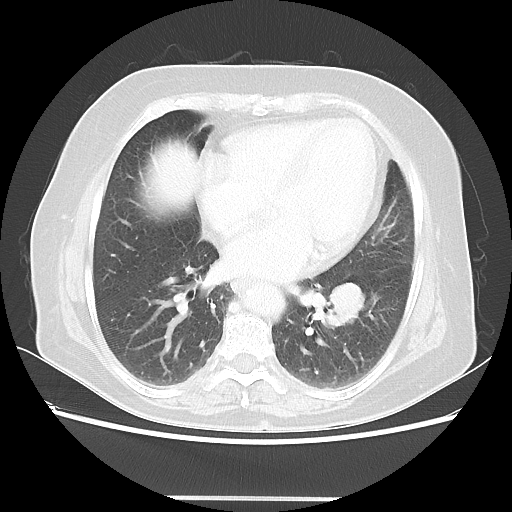
Chest CT, one axial slice; position 24 of 56 along the scan axis; lung window (W 1500 / L -600 HU); 512 × 512 image matrix, field of view 360 × 360 mm. Female patient, age 73 years. From the clinical record (not read from this slice): clinical TNM (as recorded): T1c N0 M0.
Structures marked on this image (rectangle marked by the reading radiologist):
- lung tumour (recorded histology: adenocarcinoma): bounding box [x1, y1, x2, y2] px = [325, 277, 374, 325]